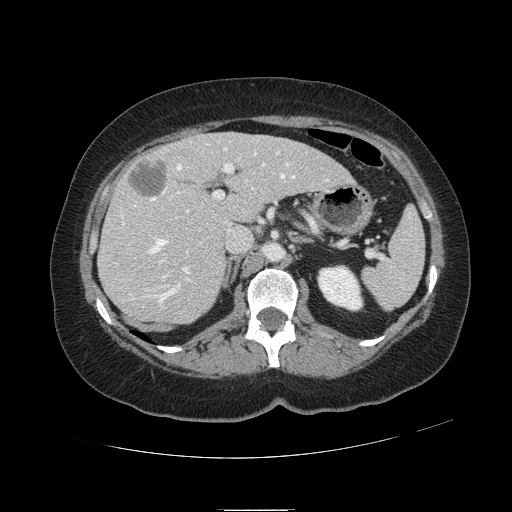
Contrast-enhanced abdominal CT, one axial slice. Position 64 of 121 along the scan axis. 120 kVp. Intravenous contrast given. Soft-tissue window (W 400 / L 40 HU). 512 × 512 image matrix, field of view 400 × 400 mm. Female patient, age 52 years. Case-level facts recorded for this patient, not image findings: diagnosis: colorectal cancer liver metastases, imaged before liver resection; multiple liver metastases: yes; largest metastasis: 6.3 cm; disease in both lobes: no.
Annotated regions visible in this slice (manually delineated by an expert):
- hepatic veins: box from (x=134, y=148) to (x=329, y=305) px
- liver: (x=99, y=133)–(x=352, y=325)
- planned liver remnant (the part of the liver to remain after resection): (x=167, y=133)–(x=353, y=222)
- portal vein (with intrahepatic branches): (x=122, y=152)–(x=279, y=278)
- liver metastasis: (x=129, y=161)–(x=167, y=196)